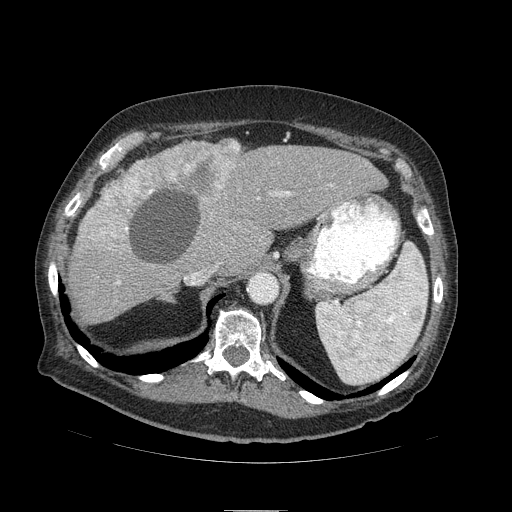
Contrast-enhanced abdominal CT (liver protocol), one axial slice. Slice 67 of 103 in the series (ordered by position). Reconstruction kernel STANDARD. 120 kVp. Soft-tissue window (W 400 / L 40 HU). 2.5 mm slice thickness. 512 × 512 image matrix. From the clinical record (not read from this slice): diagnosis: hepatocellular carcinoma (patient treated with transarterial chemoembolisation; whether this scan precedes or follows treatment is not stated here); TNM stage (as recorded): Stage-IIIA; Child-Pugh class: B; tumour size: 13 cm.
Annotated regions visible in this slice (semi-automatic segmentation, software-assisted and operator-edited):
- liver parenchyma outside the tumour (the mass and vessels are separate outlines, so this box may not span the whole liver): bounding box (x1, y1, x2, y2) in pixels: (68, 140, 388, 324)
- mass: (79, 137, 241, 254)
- liver vessels: (286, 191, 289, 194)